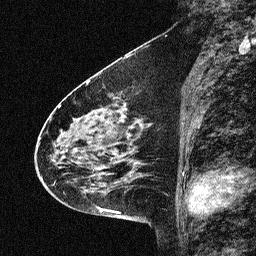
Breast MRI (dynamic contrast-enhanced), one sagittal slice. Position 27 of 64 along the scan axis. Dynamic contrast-enhanced study with each time point stored as its own series, time point 2 of 3 at this slice position (early post-contrast, ordered by acquisition time). 1.5 T. TE 4.5 ms, TR 11 ms. 2.06 mm slice thickness. 256 × 256 image matrix, field of view 200 × 200 mm. Female patient, age 46 years. Case-level facts recorded for this patient, not image findings: setting: breast cancer imaged before/during neoadjuvant chemotherapy; receptor status: HER2-positive.
Structures marked on this image (semi-automatically segmented with operator editing):
- analysis volume of interest (the breast-tissue region the enhancement analysis was run in; not a lesion): bounding box (x1, y1, x2, y2) in pixels: (42, 80, 150, 180)
- tumour enhancement mask (voxels above the 90 % enhancement threshold inside the analysis volume of interest): (55, 104, 142, 180)